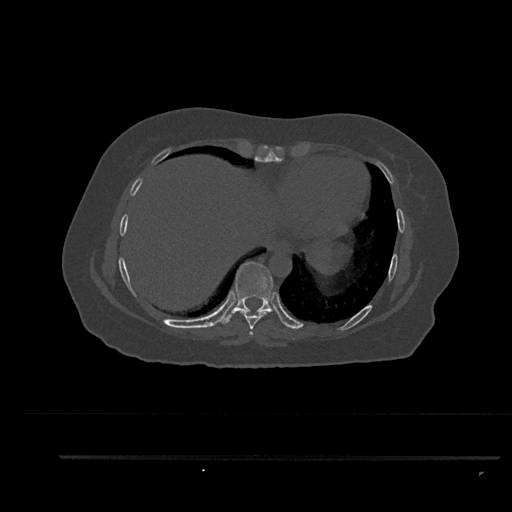
CT including the spine, one axial slice. Slice 436 of 797 in the series (ordered by position). Reconstruction kernel Br40s/3. 120 kVp. Bone window (W 1800 / L 400 HU). 0.5 mm slice thickness. 512 × 512 image matrix, field of view 408 × 408 mm. Female patient, age 44 years. Case-level facts recorded for this patient, not image findings: primary cancer: renal; vertebrae with lytic lesions (as recorded): L1.
Structures marked on this image (semi-automatically segmented with operator editing):
- T7 vertebra: bounding box (x1, y1, x2, y2) in pixels: (249, 331, 253, 335)
- T8 vertebra: (237, 309, 269, 330)
- T9 vertebra: (222, 262, 273, 325)